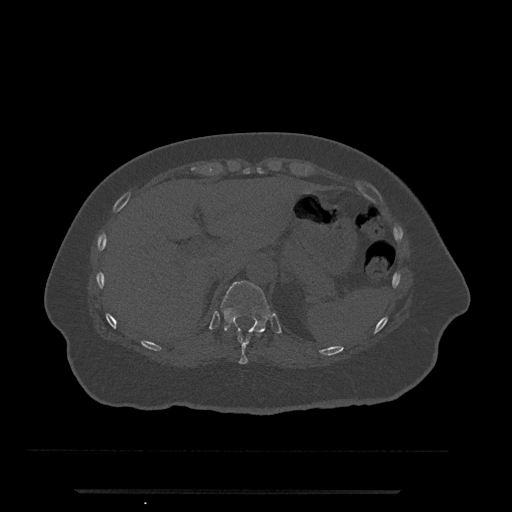
CT including the spine, one axial slice. Position 250 of 797 along the scan axis. Reconstruction kernel Br40s/3. 120 kVp. Bone window (W 1800 / L 400 HU). 0.5 mm slice thickness. 512 × 512 image matrix, field of view 440 × 440 mm. Female patient, age 51 years. From the clinical record (not read from this slice): primary cancer: neuro; vertebrae with lytic lesions (as recorded): T8.
Structures marked on this image (semi-automatic segmentation, software-assisted and operator-edited):
- T10 vertebra: bounding box [x1, y1, x2, y2] px = [238, 334, 261, 365]
- T11 vertebra: [221, 281, 270, 335]